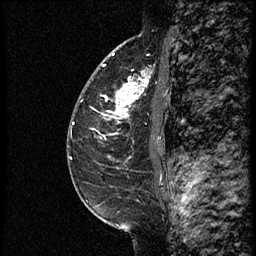
Breast MRI (dynamic contrast-enhanced), one sagittal slice; slice 39 of 60 in the series (ordered by position); dynamic contrast-enhanced study with each time point stored as its own series, time point 2 of 3 at this slice position (early post-contrast, ordered by acquisition time); 1.5 T; TE 4.2 ms, TR 18.9 ms; 2 mm slice thickness; 256 × 256 image matrix. Female patient. From the clinical record (not read from this slice): setting: breast cancer imaged before/during neoadjuvant chemotherapy; receptor status: HER2-positive.
Annotated regions visible in this slice (semi-automatic segmentation, software-assisted and operator-edited):
- analysis volume of interest (the breast-tissue region the enhancement analysis was run in; not a lesion): bounding box <92,66,161,147> (left, top, right, bottom; pixels)
- tumour enhancement mask (voxels above the 100 % enhancement threshold inside the analysis volume of interest): <105,73,161,141>